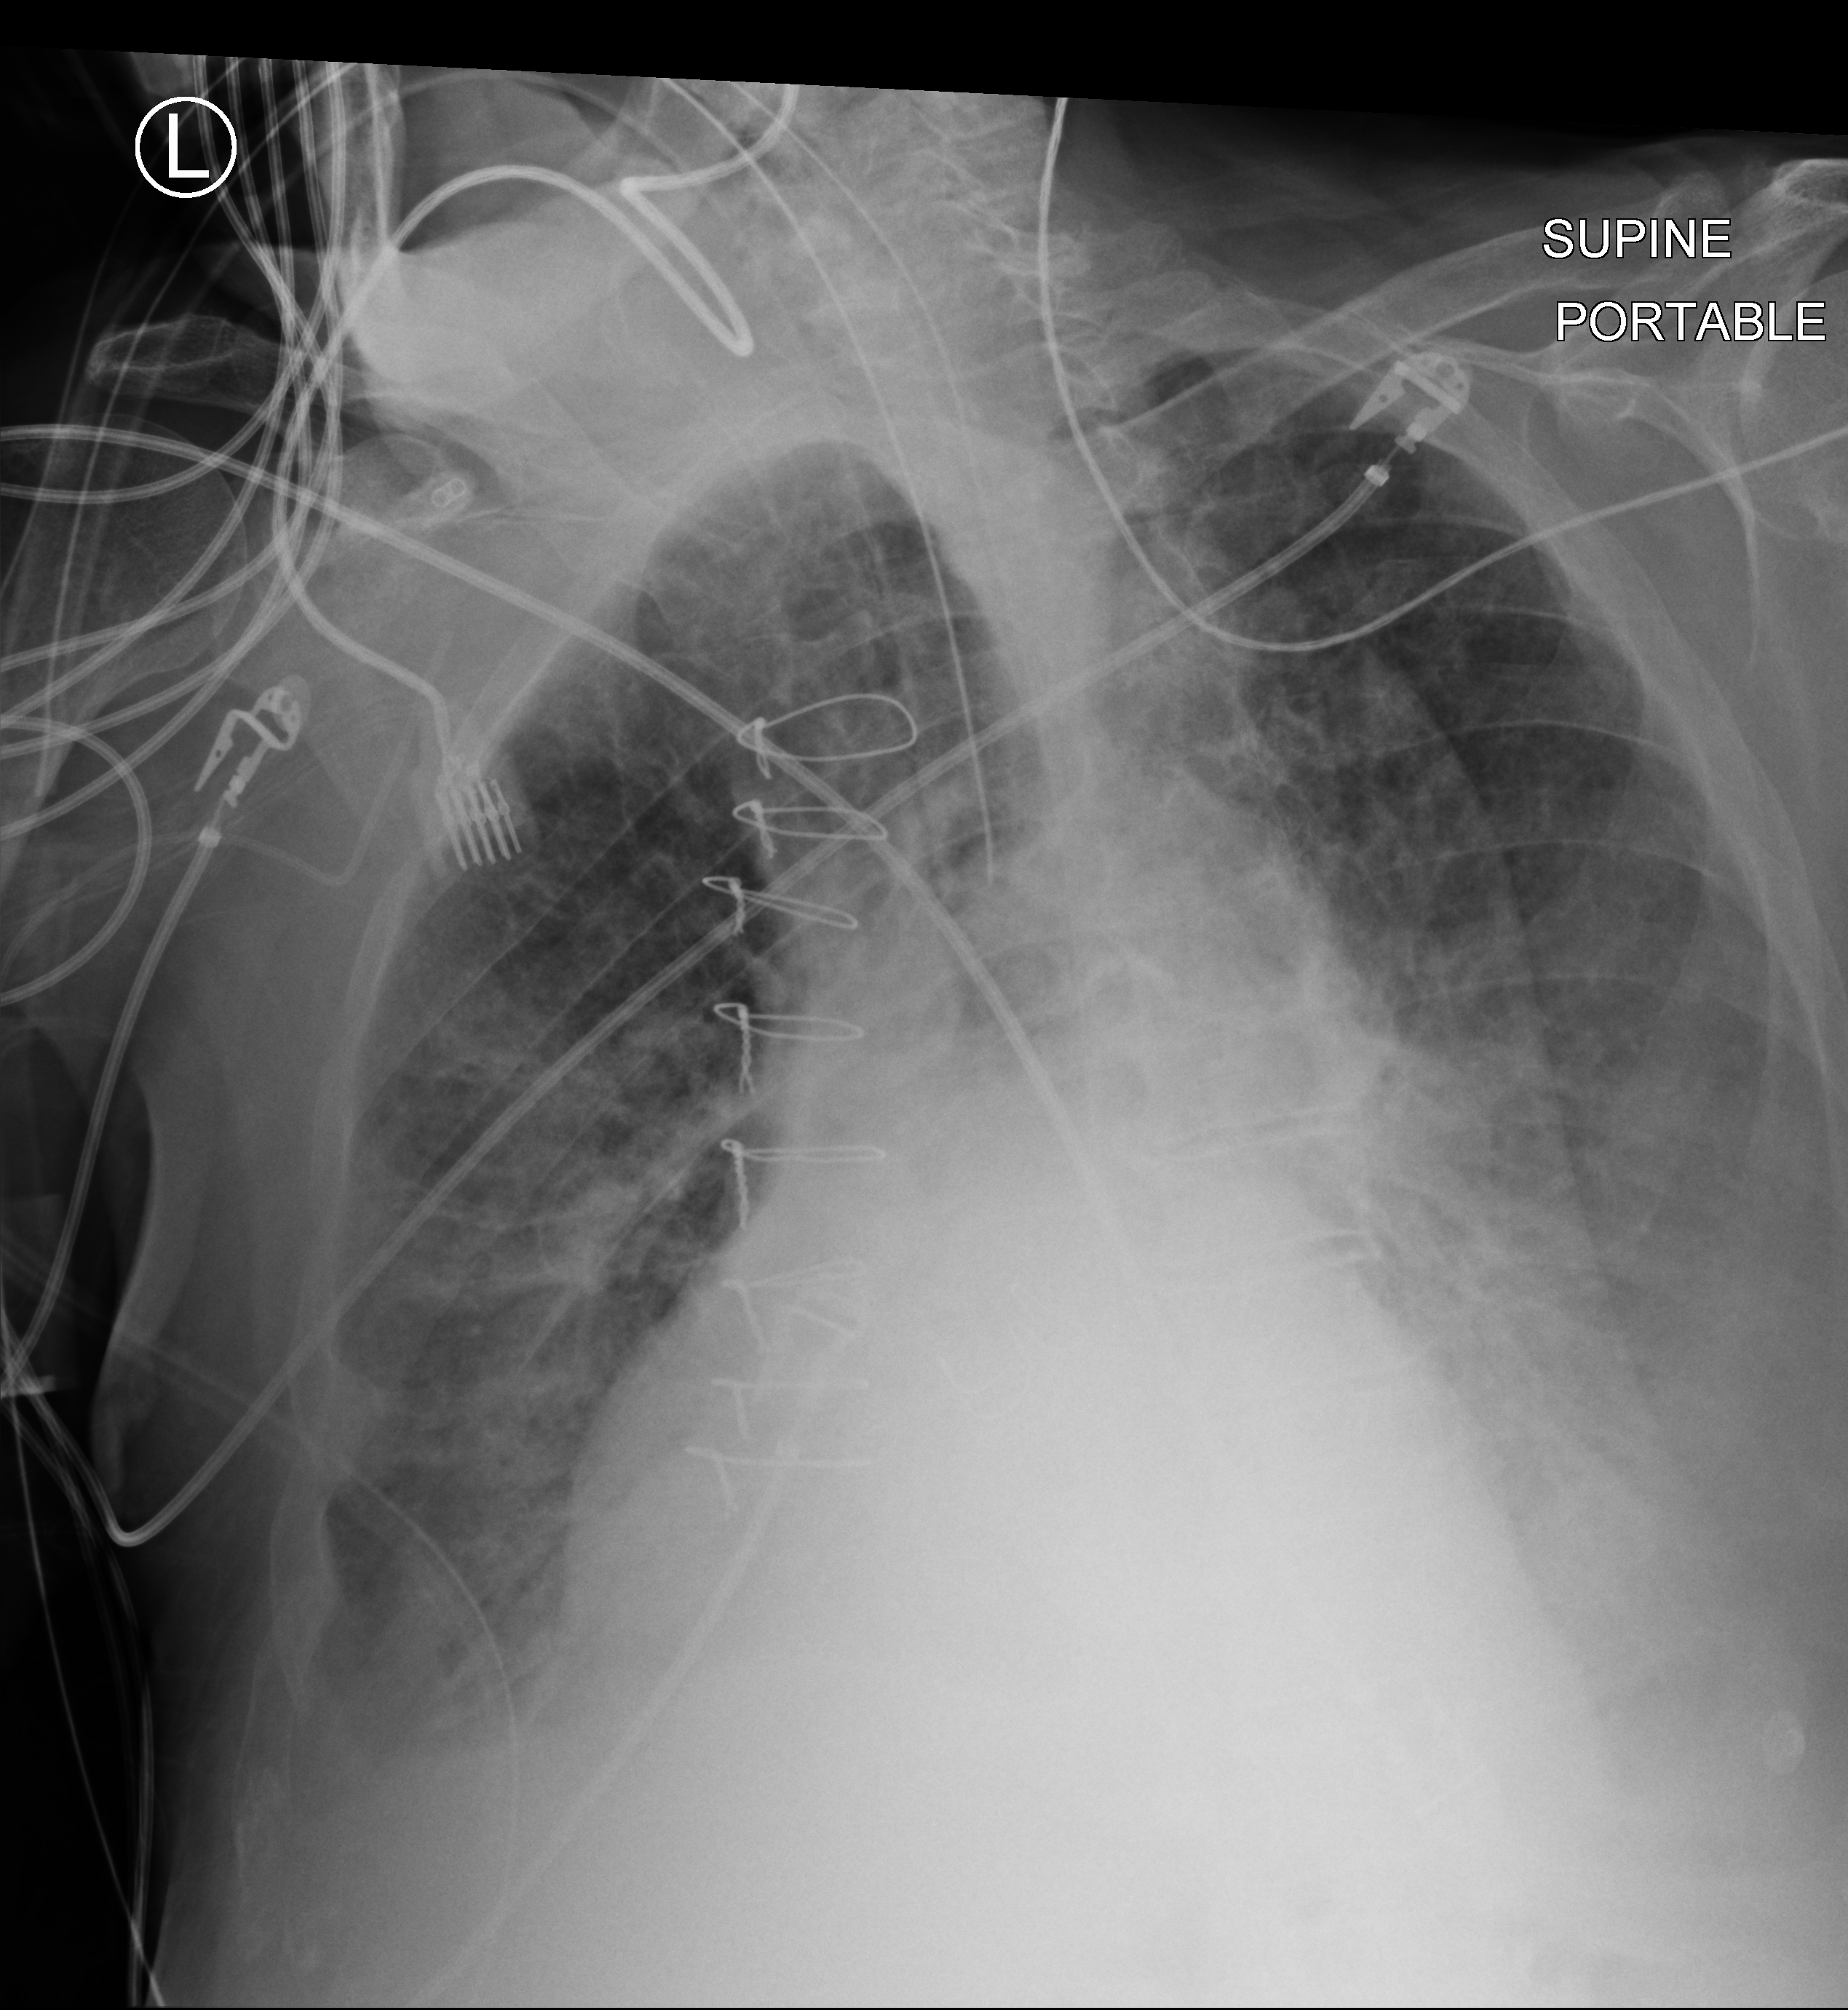
Portable chest radiograph, anteroposterior (AP) projection. Male patient hospitalised with COVID-19, age 75–90 years.
From the hospital-stay record, not from the radiograph (when in the stay this image was taken is not recorded):
- admitted to intensive care during this hospital stay: yes